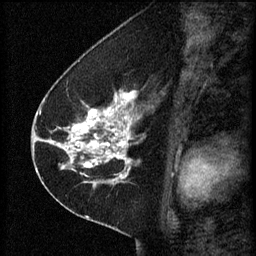
Breast MRI (dynamic contrast-enhanced), one sagittal slice; 3 images stored at this slice position (order not interpretable as contrast timing); 1.5 T; TE 4.2 ms, TR 8.2 ms; 256 × 256 image matrix, field of view 180 × 180 mm. Patient: female, 41 years.
Outlined on this slice (semi-automatically segmented with operator editing):
- analysis volume of interest (the breast-tissue region the enhancement analysis was run in; not a lesion): bounding box (x1, y1, x2, y2) in pixels: (67, 92, 165, 173)
- tumour enhancement mask (voxels above the 70 % enhancement threshold inside the analysis volume of interest): (67, 92, 140, 173)